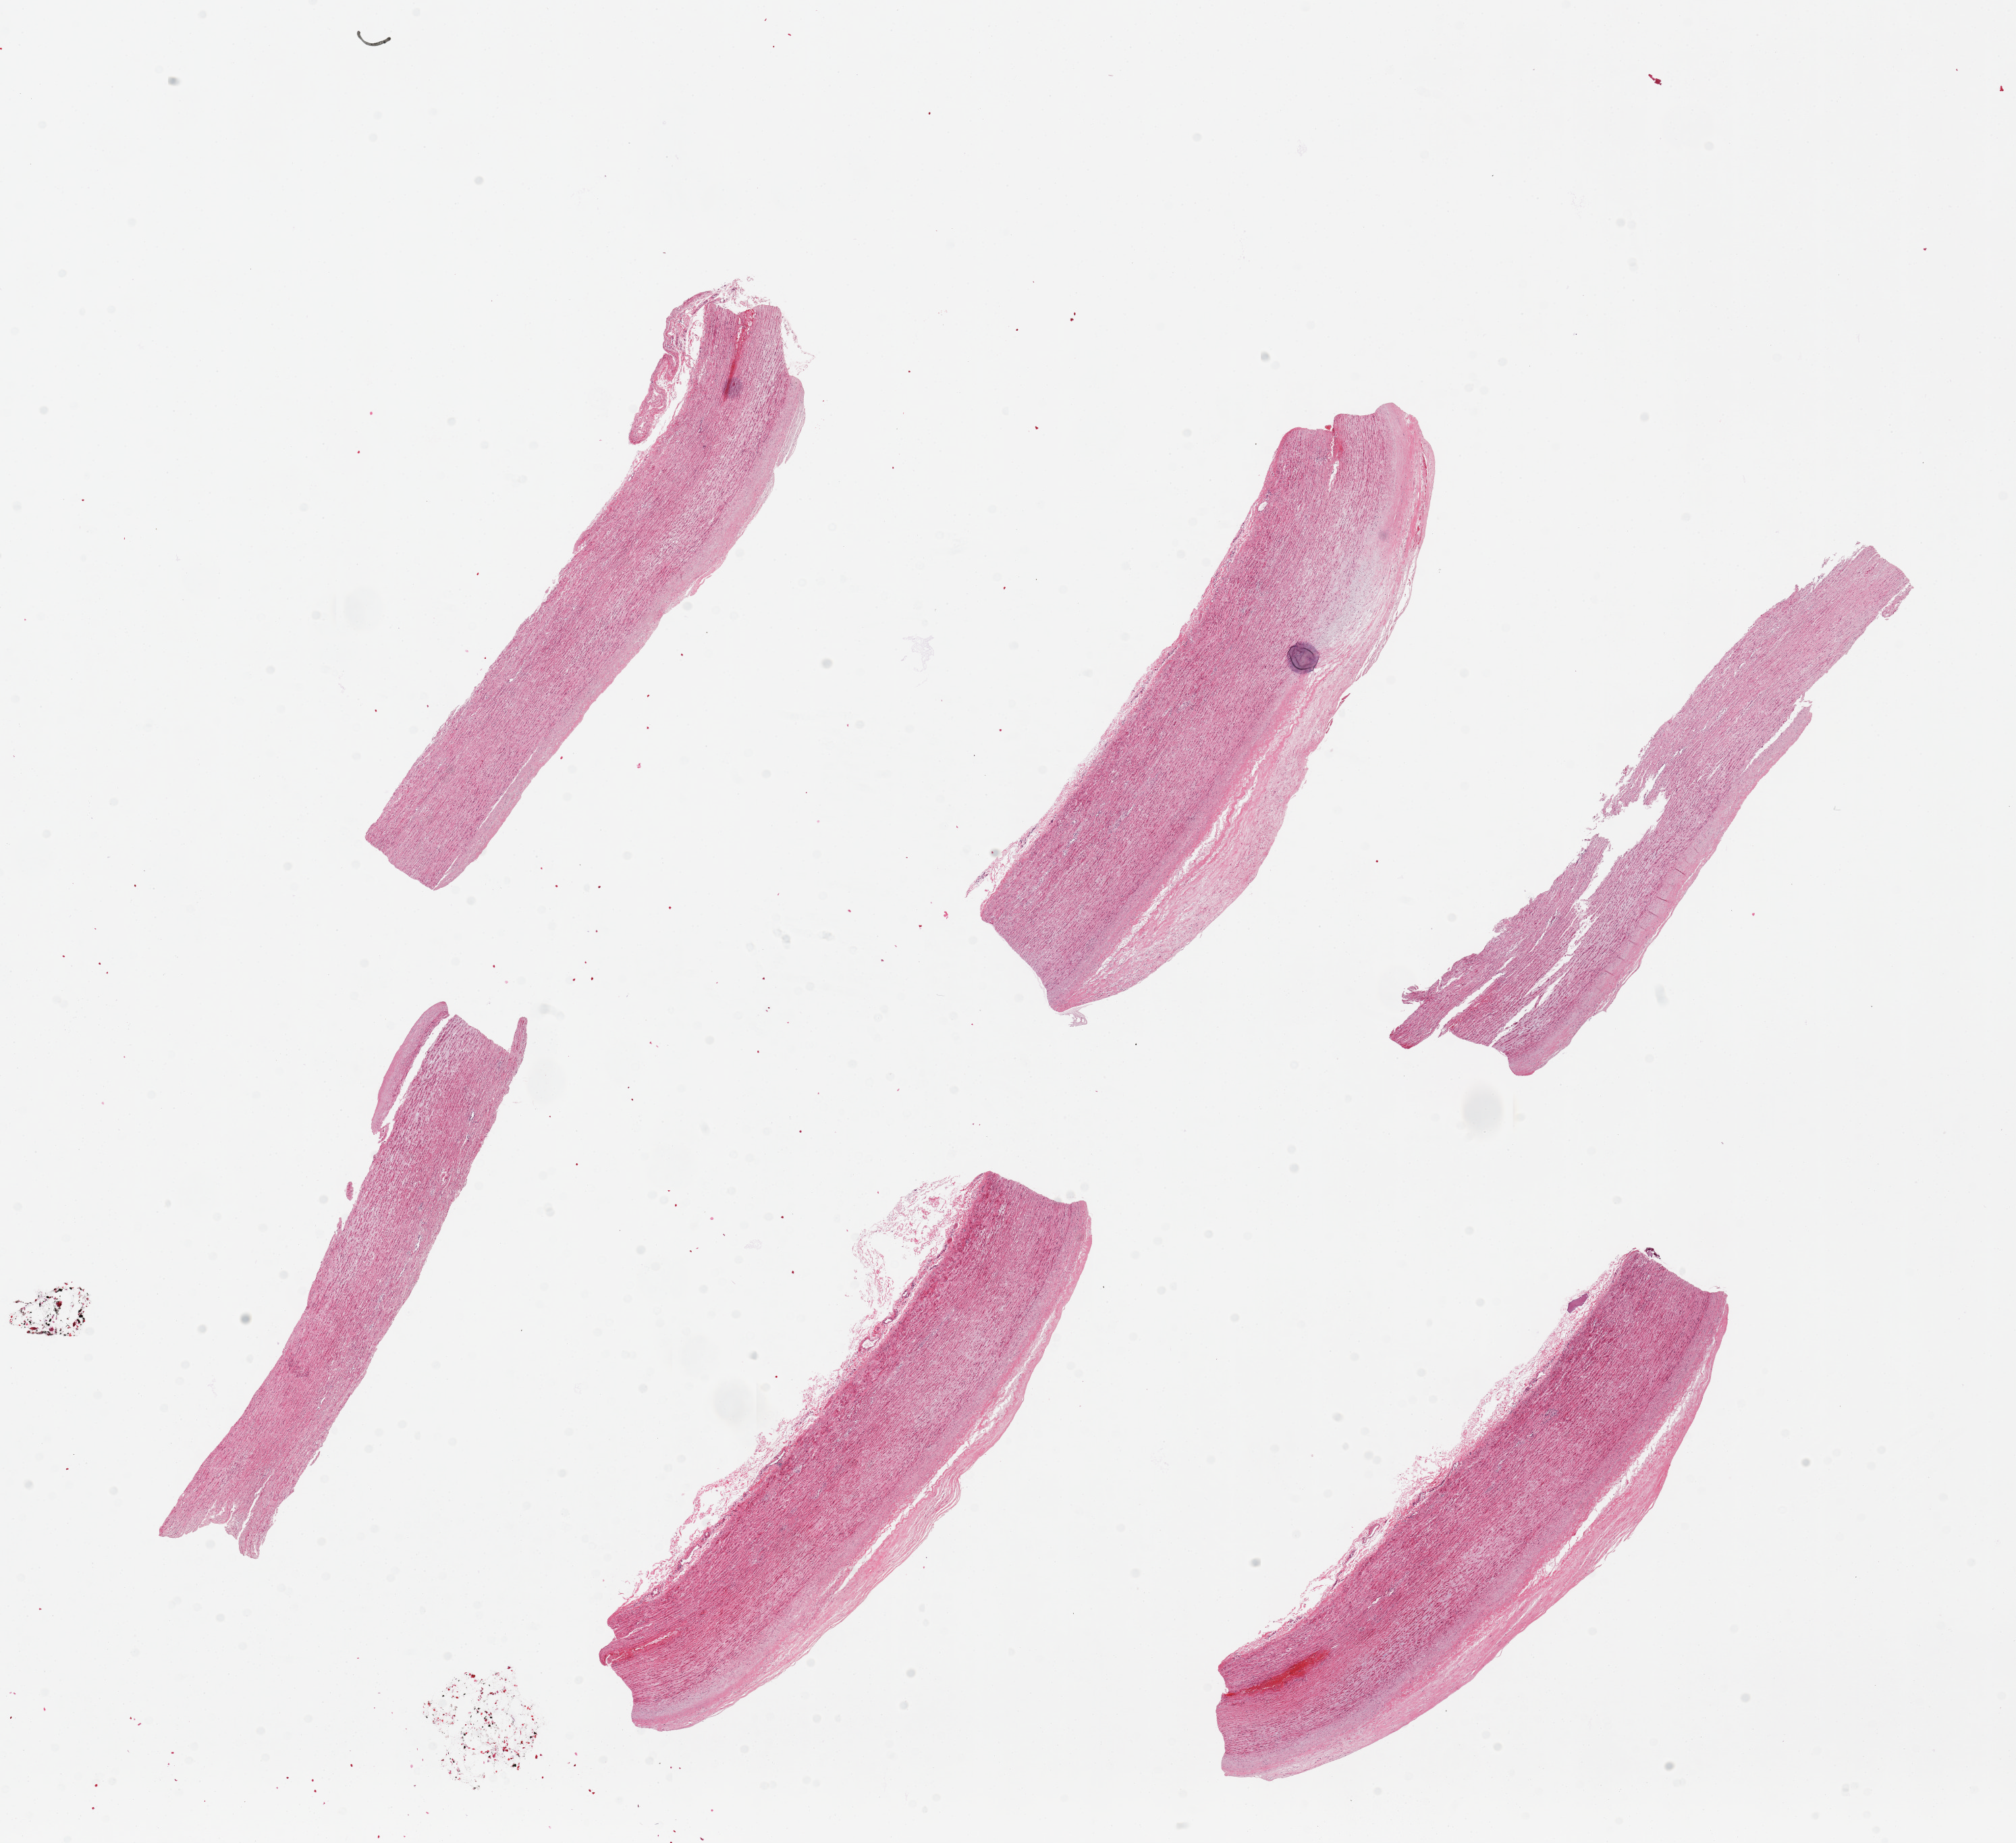
Whole-slide image, H&E stain, whole scanned area (about 23.6 x 21.6 mm) shown as a low-resolution overview, PAXgene-fixed, paraffin-embedded tissue, target tissue: aorta, tissue donor sample.
• pathologist's review note for this sample: 6 pieces, up to 8x2mm; well dissected; flat plaques